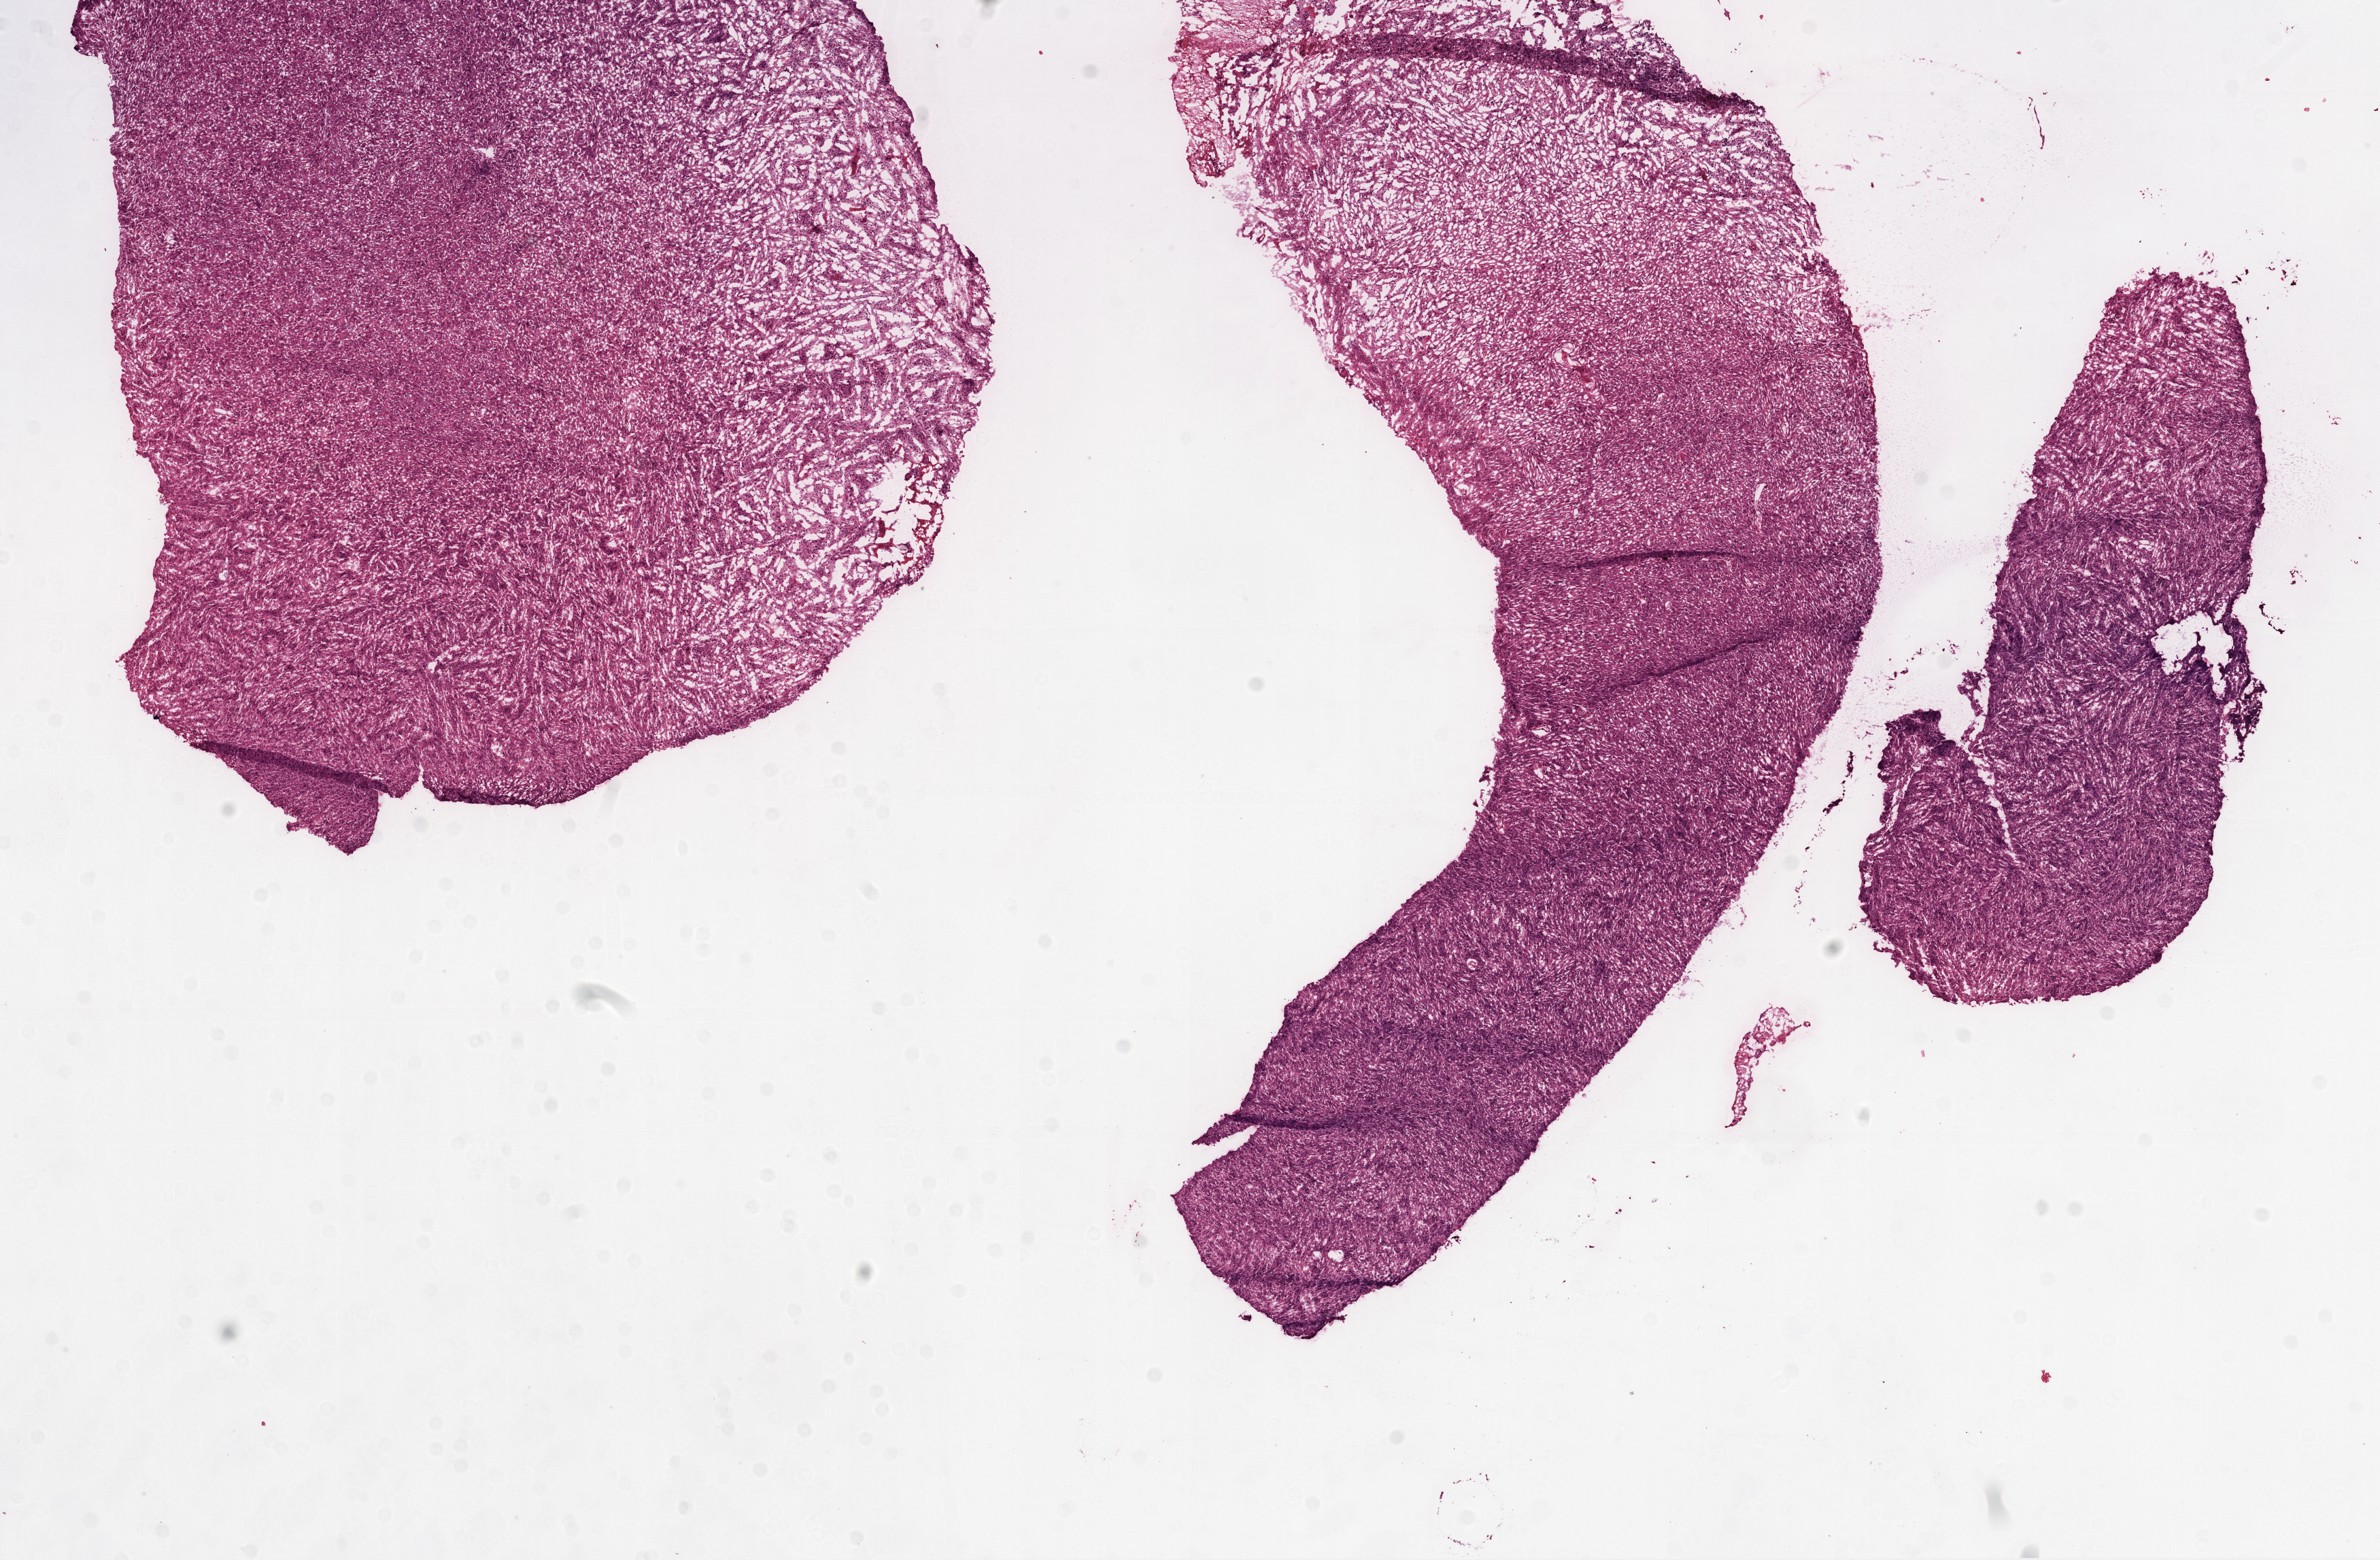
Digitized Hematoxylin and eosin (H&E) stained tissue section (whole slide), a low-resolution overview of the entire scanned area, about 14.0 x 9.2 mm (slide scanned at 20x), frozen section from the top of the tissue portion, sample: primary tumour, brain. Female, age 52 years at initial diagnosis.
Pathologic diagnosis: Glioblastoma.